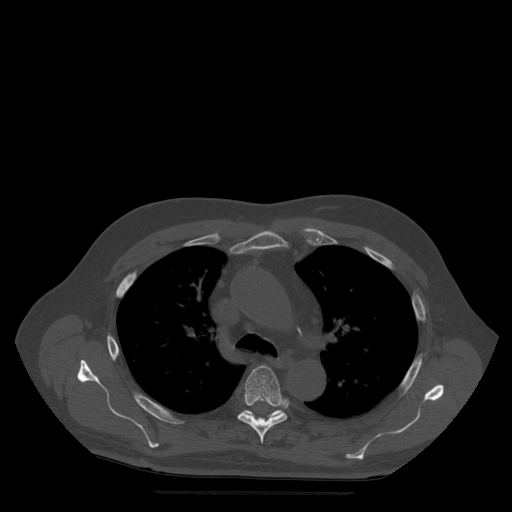
CT including the spine, one axial slice. Slice 370 of 522 in the series (ordered by position). Bone window (W 1800 / L 400 HU). 1.25 mm slice thickness. 512 × 512 image matrix. Patient age 72 years. From the clinical record (not read from this slice): primary cancer: prostate.
Outlined on this slice (semi-automatically segmented with operator editing):
- T5 vertebra: bounding box <238,366,289,444> (left, top, right, bottom; pixels)
- T6 vertebra: <245,411,280,421>